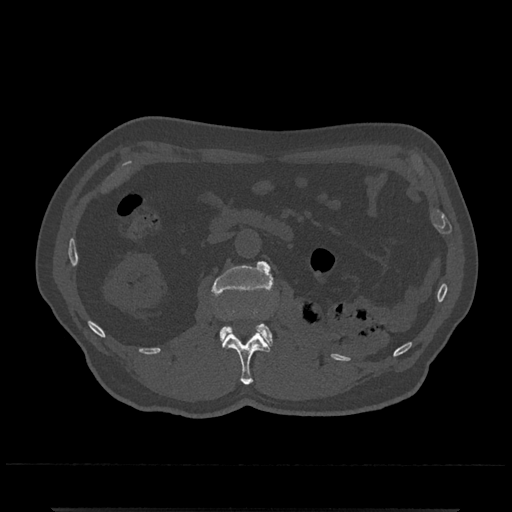
CT including the spine, one axial slice; position 329 of 797 along the scan axis; bone window (W 1800 / L 400 HU); 0.5 mm slice thickness; 512 × 512 image matrix. Patient: male, 67 years. From the clinical record (not read from this slice): primary cancer: prostate.
Structures marked on this image (semi-automatically segmented with operator editing):
- L1 vertebra: bounding box (x1, y1, x2, y2) in pixels: (223, 331, 270, 385)
- L2 vertebra: (211, 261, 274, 347)